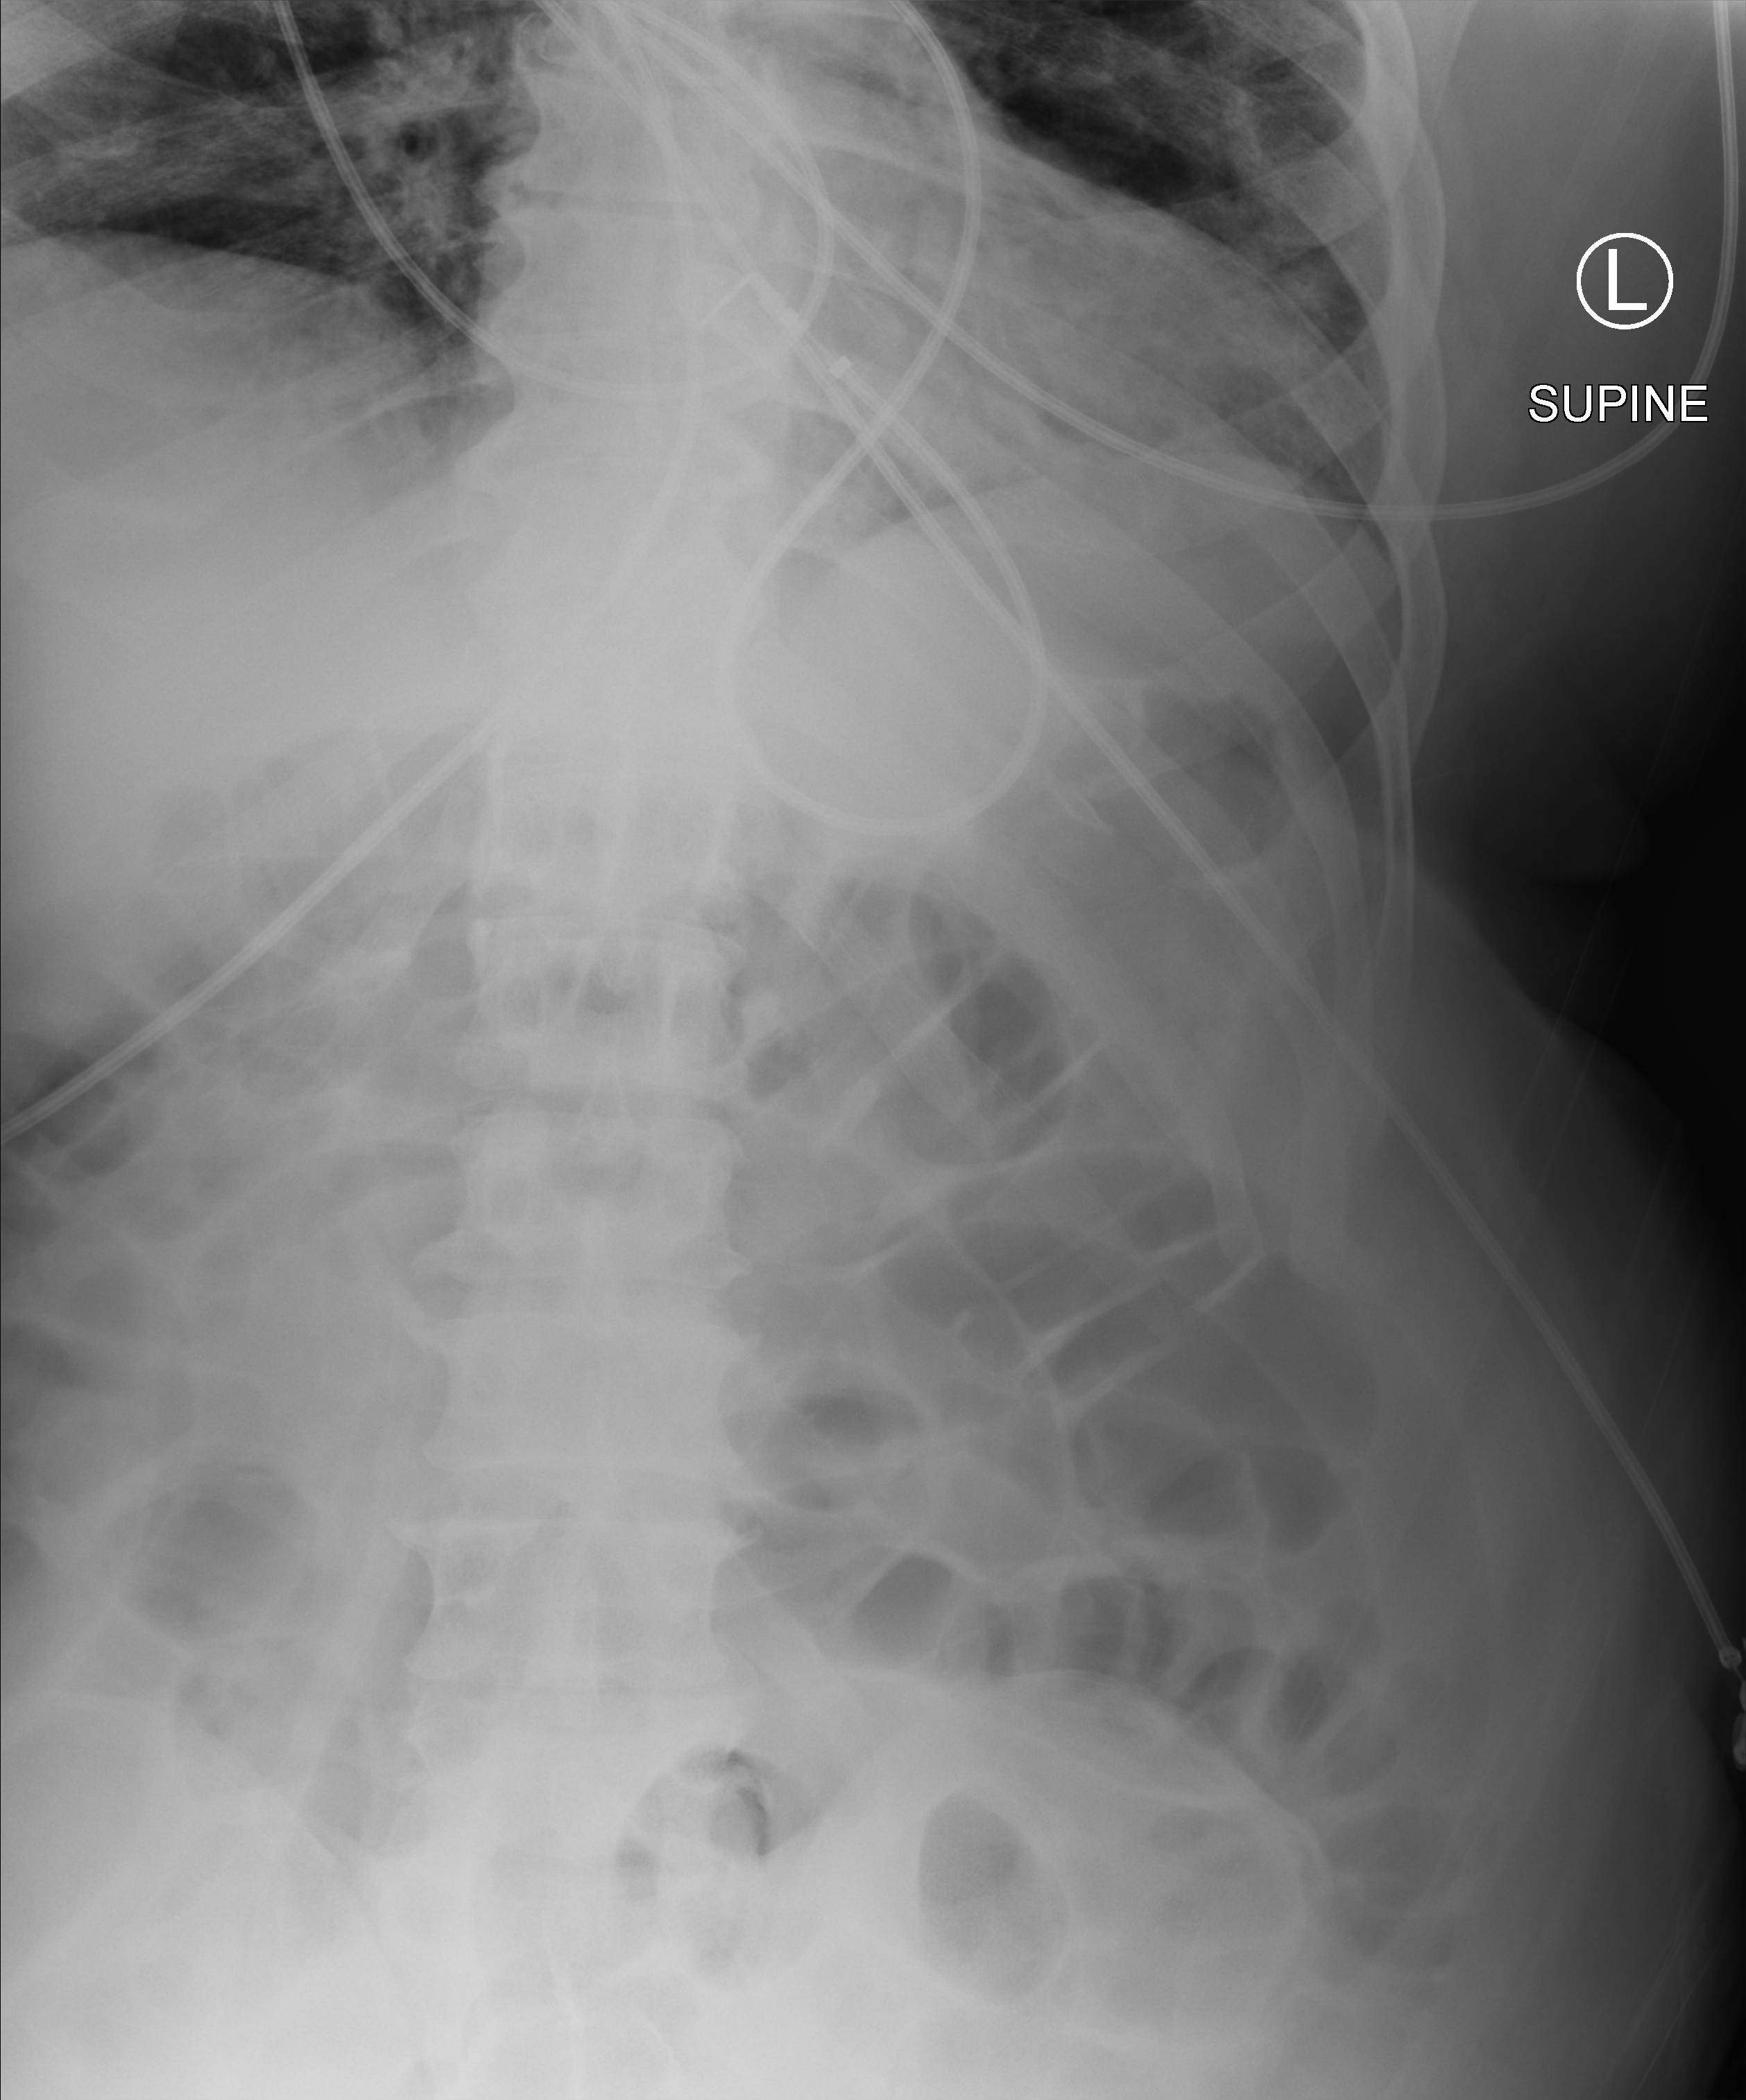
Portable abdomen radiograph; anteroposterior (AP) projection. Male patient hospitalised with COVID-19, age 18–59 years.
Admission-level facts for this patient (not findings on this image; timing relative to this image not recorded): hypertension (admission record): no; mechanically ventilated during this hospital stay: yes; other chronic lung disease (admission record): no.